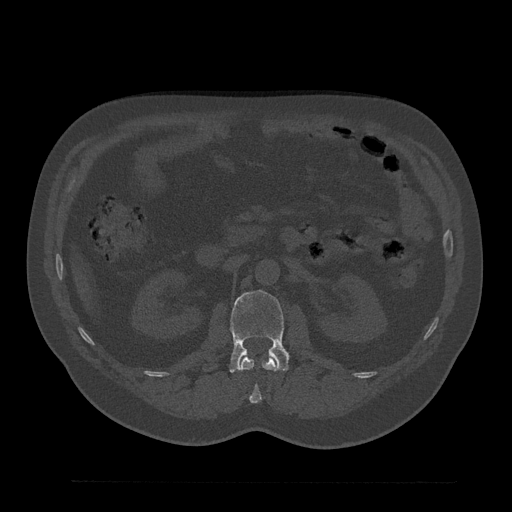
CT including the spine, one axial slice. Position 122 of 797 along the scan axis. Reconstruction kernel Br40s/3. 120 kVp. Bone window (W 1800 / L 400 HU). 0.5 mm slice thickness. 512 × 512 image matrix, field of view 430 × 430 mm. Patient: male, 61 years. Case-level facts recorded for this patient, not image findings: primary cancer: prostate.
Structures marked on this image (semi-automatically segmented with operator editing):
- L1 vertebra: box from (x=240, y=355) to (x=278, y=404) px
- L2 vertebra: (x=229, y=290)–(x=289, y=372)